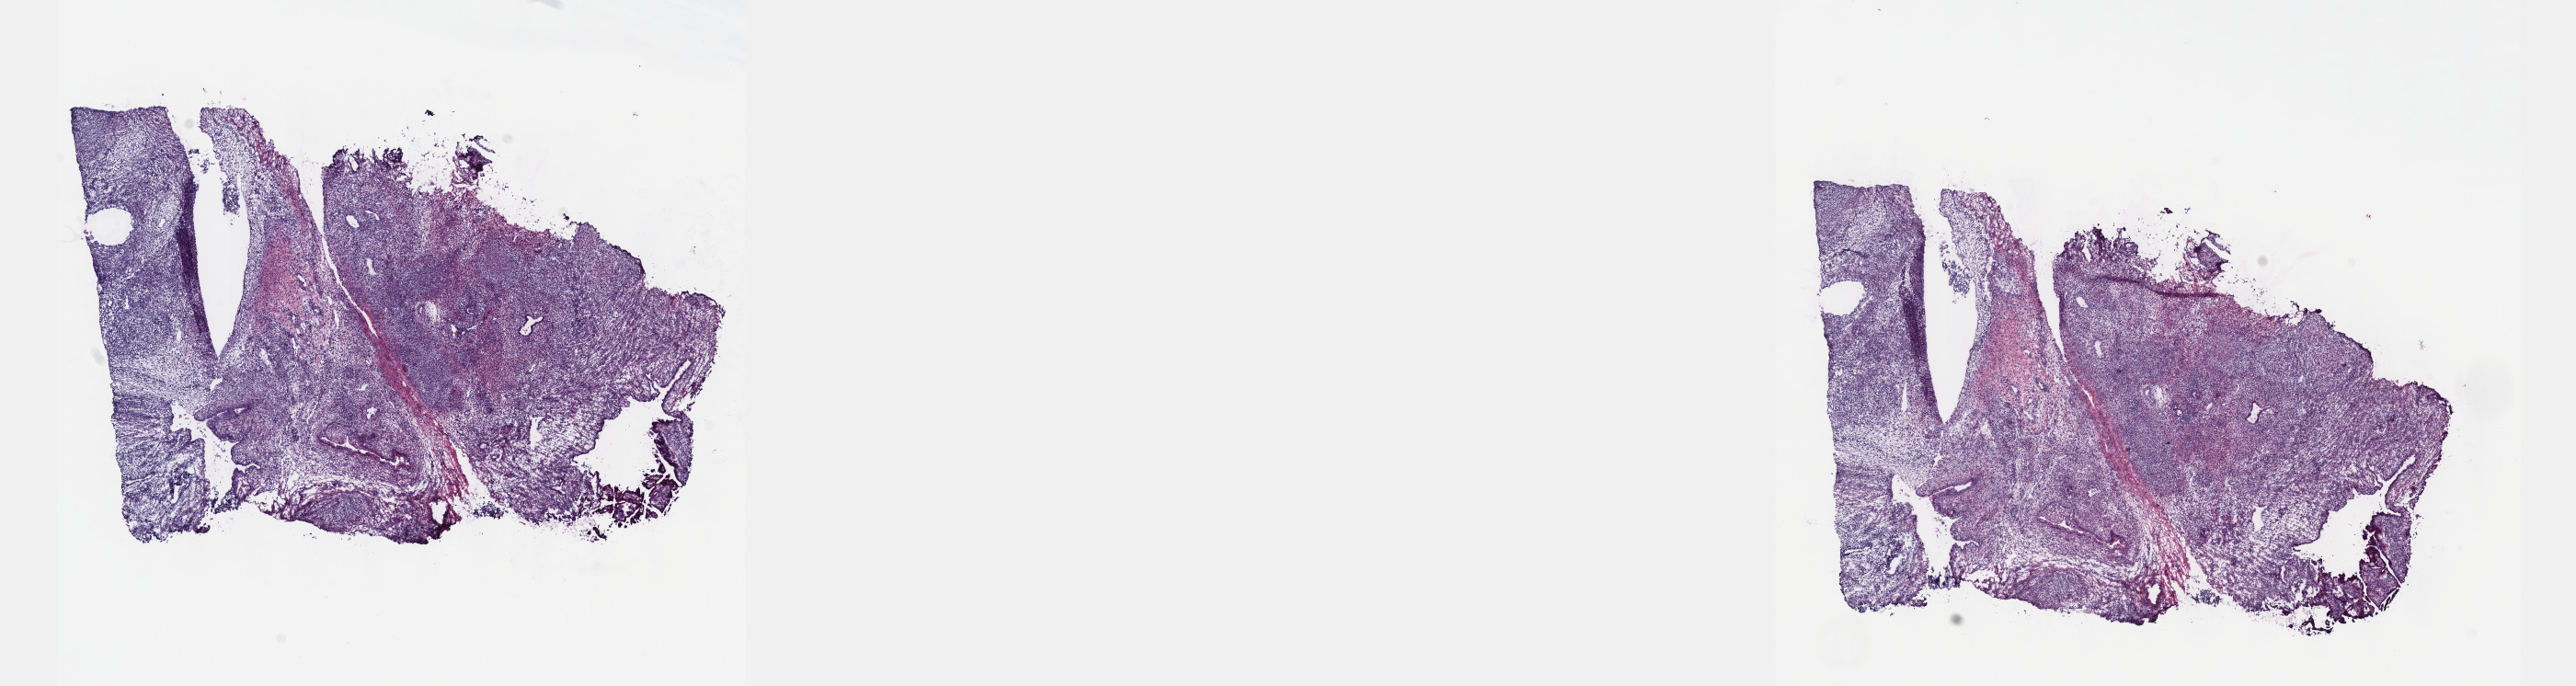
Hematoxylin and eosin (H&E) stained whole-slide image — low-resolution overview of the scanned area, about 22.6 x 6.0 mm. Male patient. Composition of this section per pathologist review: tumour cells 90%, tumour nuclei 95%, normal cells 0%, stromal cells 10%, necrosis 0%. Infiltration values recorded for this section: lymphocyte infiltration 0%, monocyte infiltration 0%, neutrophil infiltration 0%.
- specimen: frozen section from the top of the tissue portion; testis, primary tumour sample